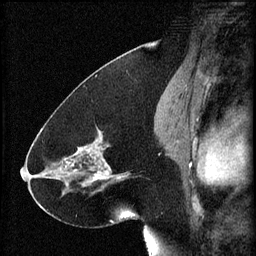
Breast MRI (dynamic contrast-enhanced), one sagittal slice; slice 33 of 60 in the series (ordered by position); 3 images stored at this slice position (order not interpretable as contrast timing); 1.5 T; TE 4.2 ms, TR 8.2 ms; 2 mm slice thickness; 256 × 256 image matrix, field of view 180 × 180 mm. Female patient, age 41 years.
Structures marked on this image (semi-automatically segmented with operator editing):
- analysis volume of interest (the breast-tissue region the enhancement analysis was run in; not a lesion): bounding box <72,124,134,195> (left, top, right, bottom; pixels)
- tumour enhancement mask (voxels above the 70 % enhancement threshold inside the analysis volume of interest): <72,132,126,187>